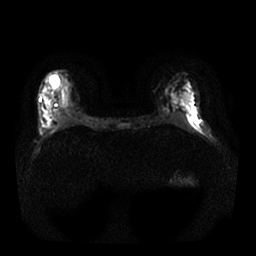
Breast MRI, one axial slice. Slice 12 of 25 in the series (ordered by position). Diffusion-weighted series; image 2 of 4 stored at this slice position (different b-values; order by instance number). 1.5 T. 256 × 256 image matrix. Female patient.
Outlined on this slice (expert manual segmentation):
- tumour on diffusion-weighted imaging: box from (x=60, y=106) to (x=72, y=117) px